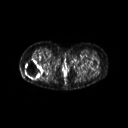
FDG PET of an extremity soft-tissue mass (from a PET/CT study), one axial slice; slice 33 of 267 in the series (ordered by position); 3.27 mm slice thickness; 128 × 128 image matrix. Patient: female, 57 years. Case-level facts recorded for this patient, not image findings: histological type: epithelioid sarcoma with vascular differentiation; site of the primary tumour: right buttock.
Annotated regions visible in this slice (expert contour drawn on MRI and transferred to this co-registered scan by the dataset authors):
- gross tumour volume (mass): bounding box (x1, y1, x2, y2) in pixels: (24, 59, 43, 78)